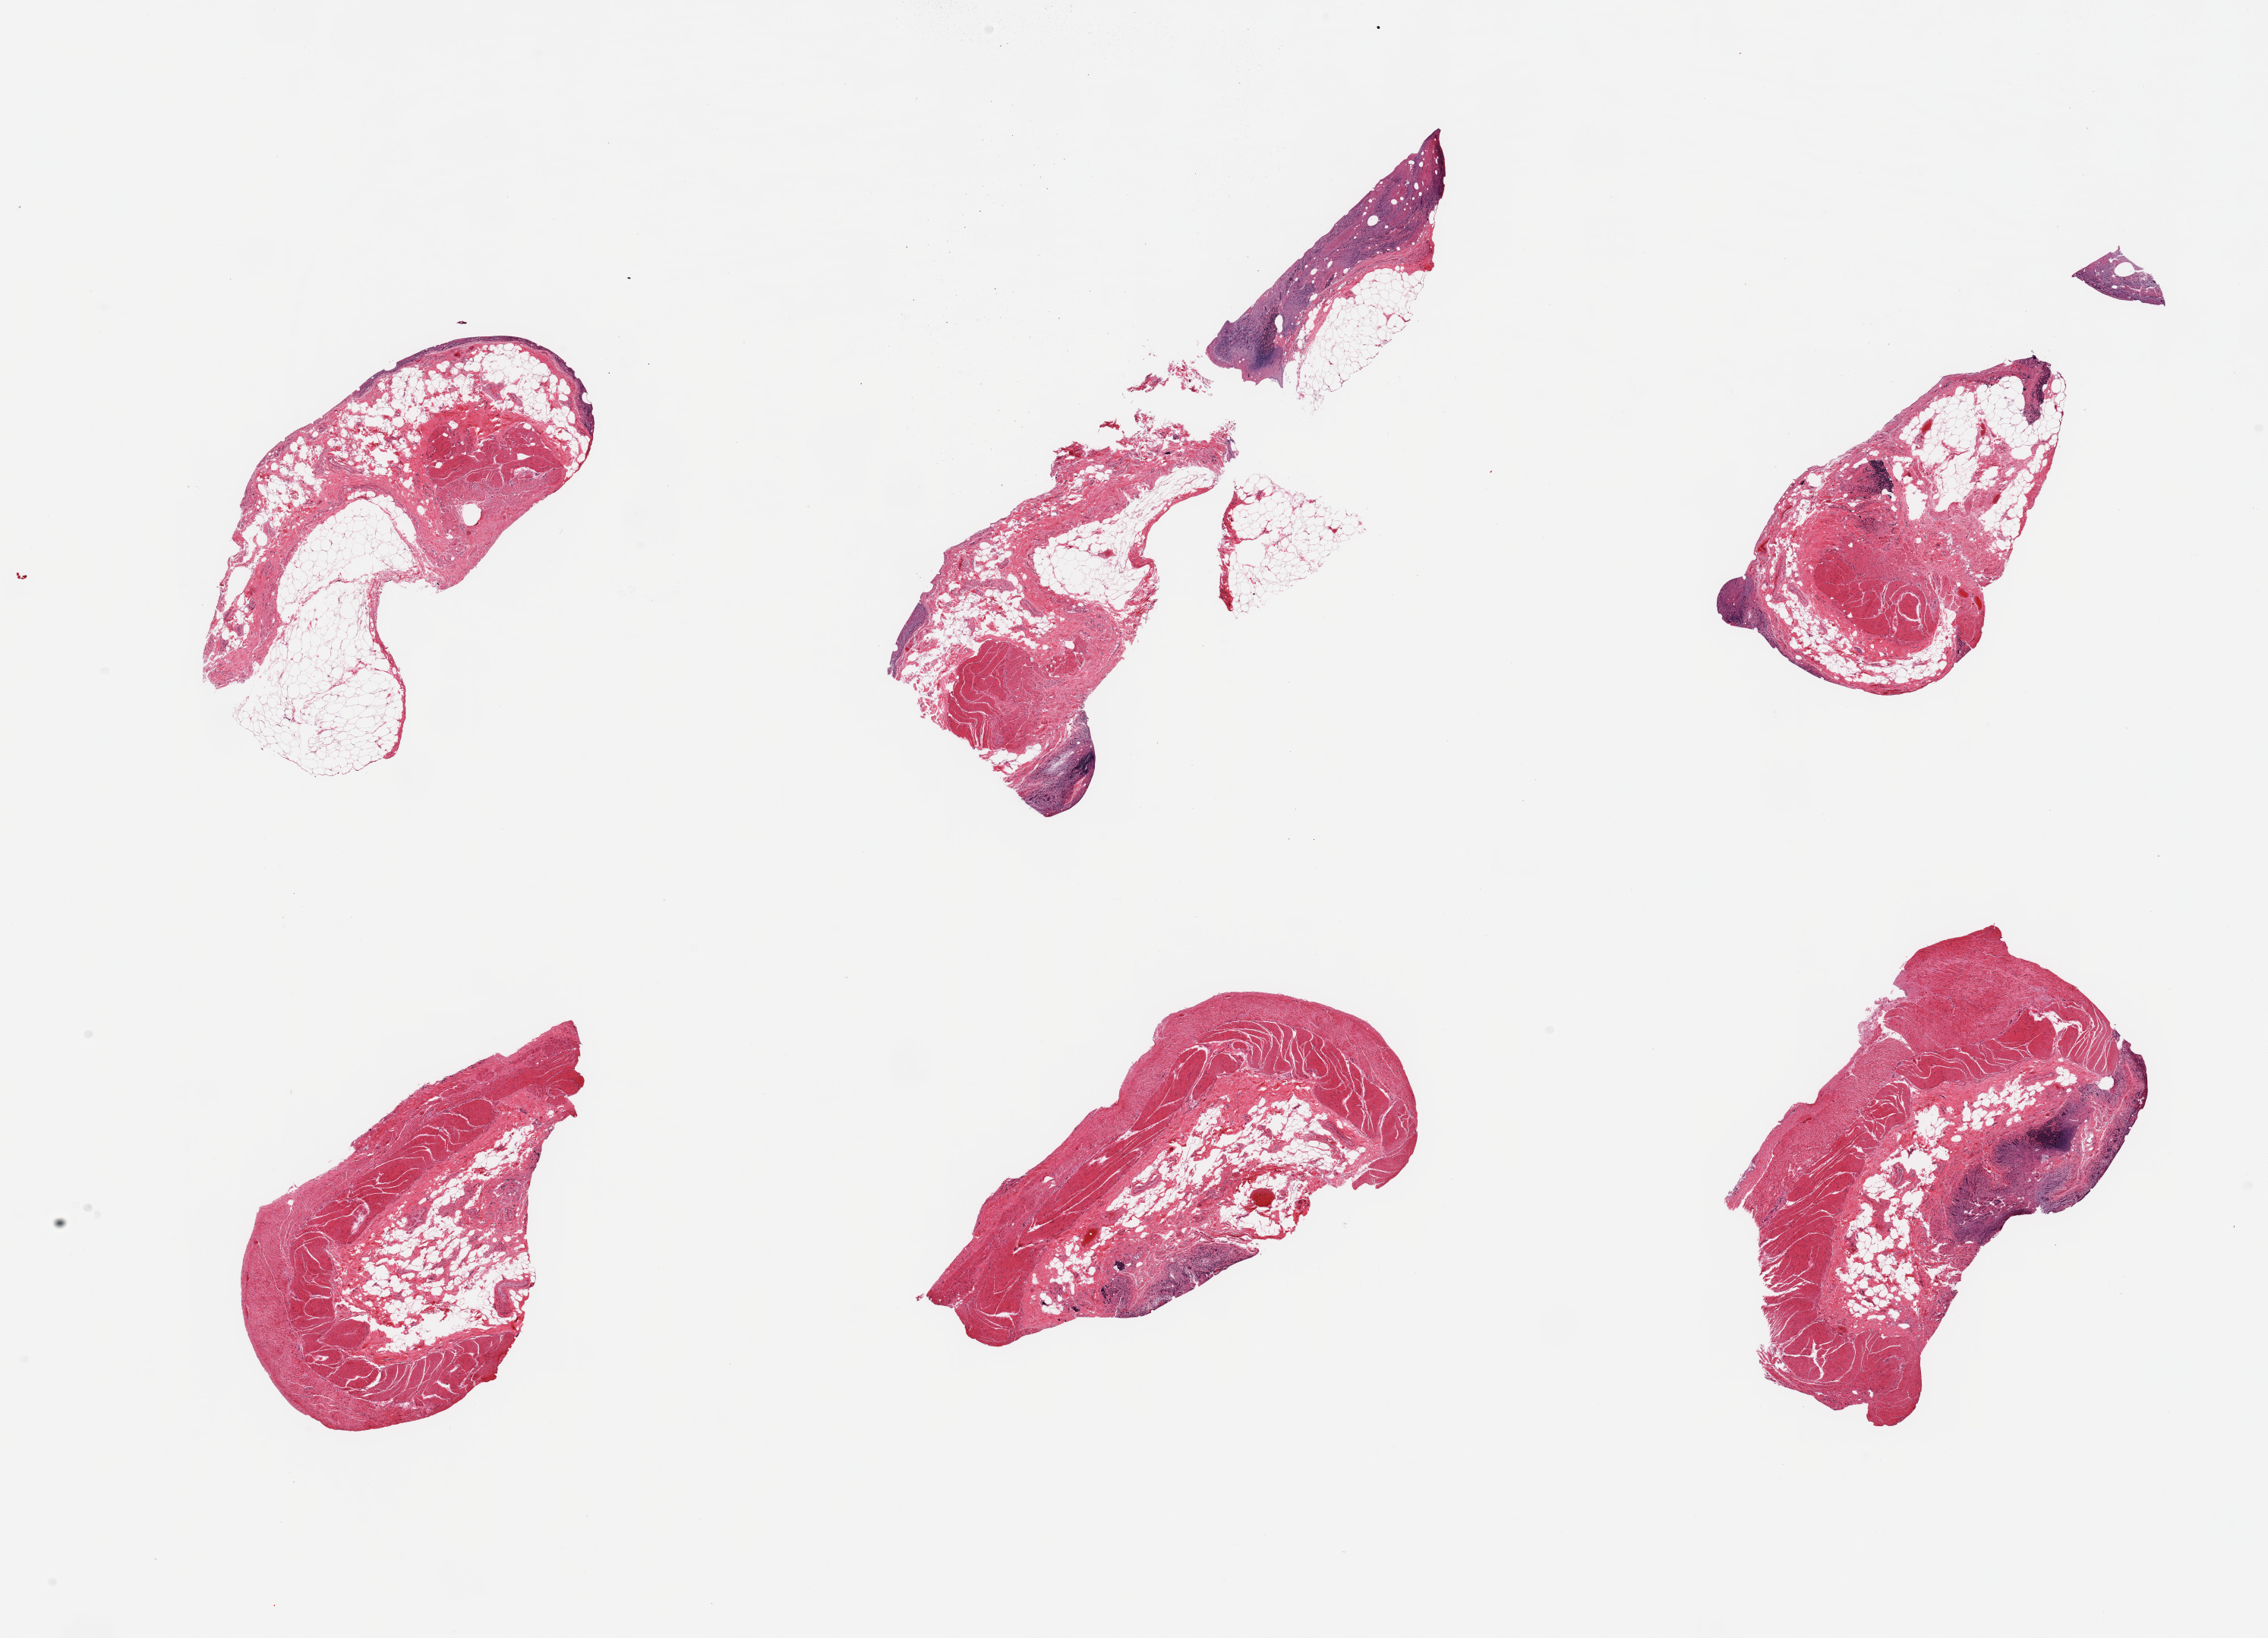
Whole-slide image, hematoxylin and eosin (H&E) stain — shown as a low-resolution overview of the whole scanned area (about 23.6 x 17.1 mm, from a 20x scan); PAXgene-fixed paraffin-embedded (PFPE) section; target tissue: ileum; tissue donor sample.
Review note (as recorded): 6 pieces; autolyzed mucosa and too few (mostly autolyzed) lymphoid aggregates to warrant analysis, muscularis is also present (not target).